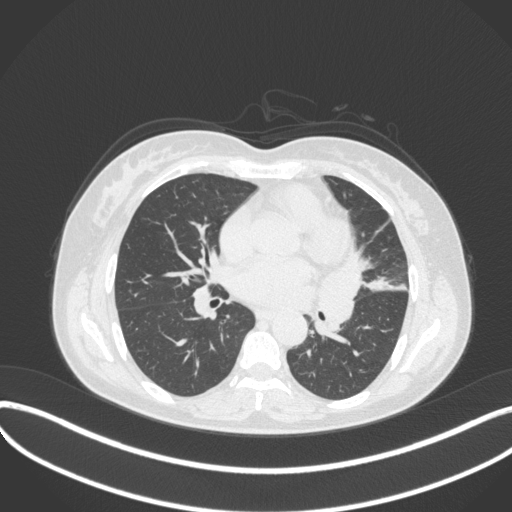
Chest CT, one axial slice. 120 kVp. Lung window (W 1500 / L -600 HU). 1 mm slice thickness. 512 × 512 image matrix. Patient: female, 54 years. From the clinical record (not read from this slice): clinical TNM (as recorded): T2a N1 M0.
Annotated regions visible in this slice (rectangle marked by the reading radiologist):
- lung tumour (recorded histology: small cell carcinoma): bounding box [x1, y1, x2, y2] px = [317, 246, 378, 340]